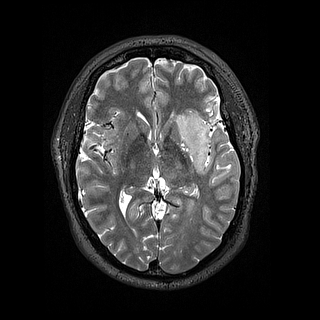
Brain MRI from a brain-tumour surgery series, one axial slice. Slice 86 of 144 in the series (ordered by position). 320 × 320 image matrix, field of view 254 × 254 mm. From the clinical record (not read from this slice): histopathology: Astrocytoma; WHO grade: 2; IDH mutation: yes.
Outlined on this slice (manually delineated by an expert):
- tumour: bounding box (x1, y1, x2, y2) in pixels: (175, 108, 211, 174)